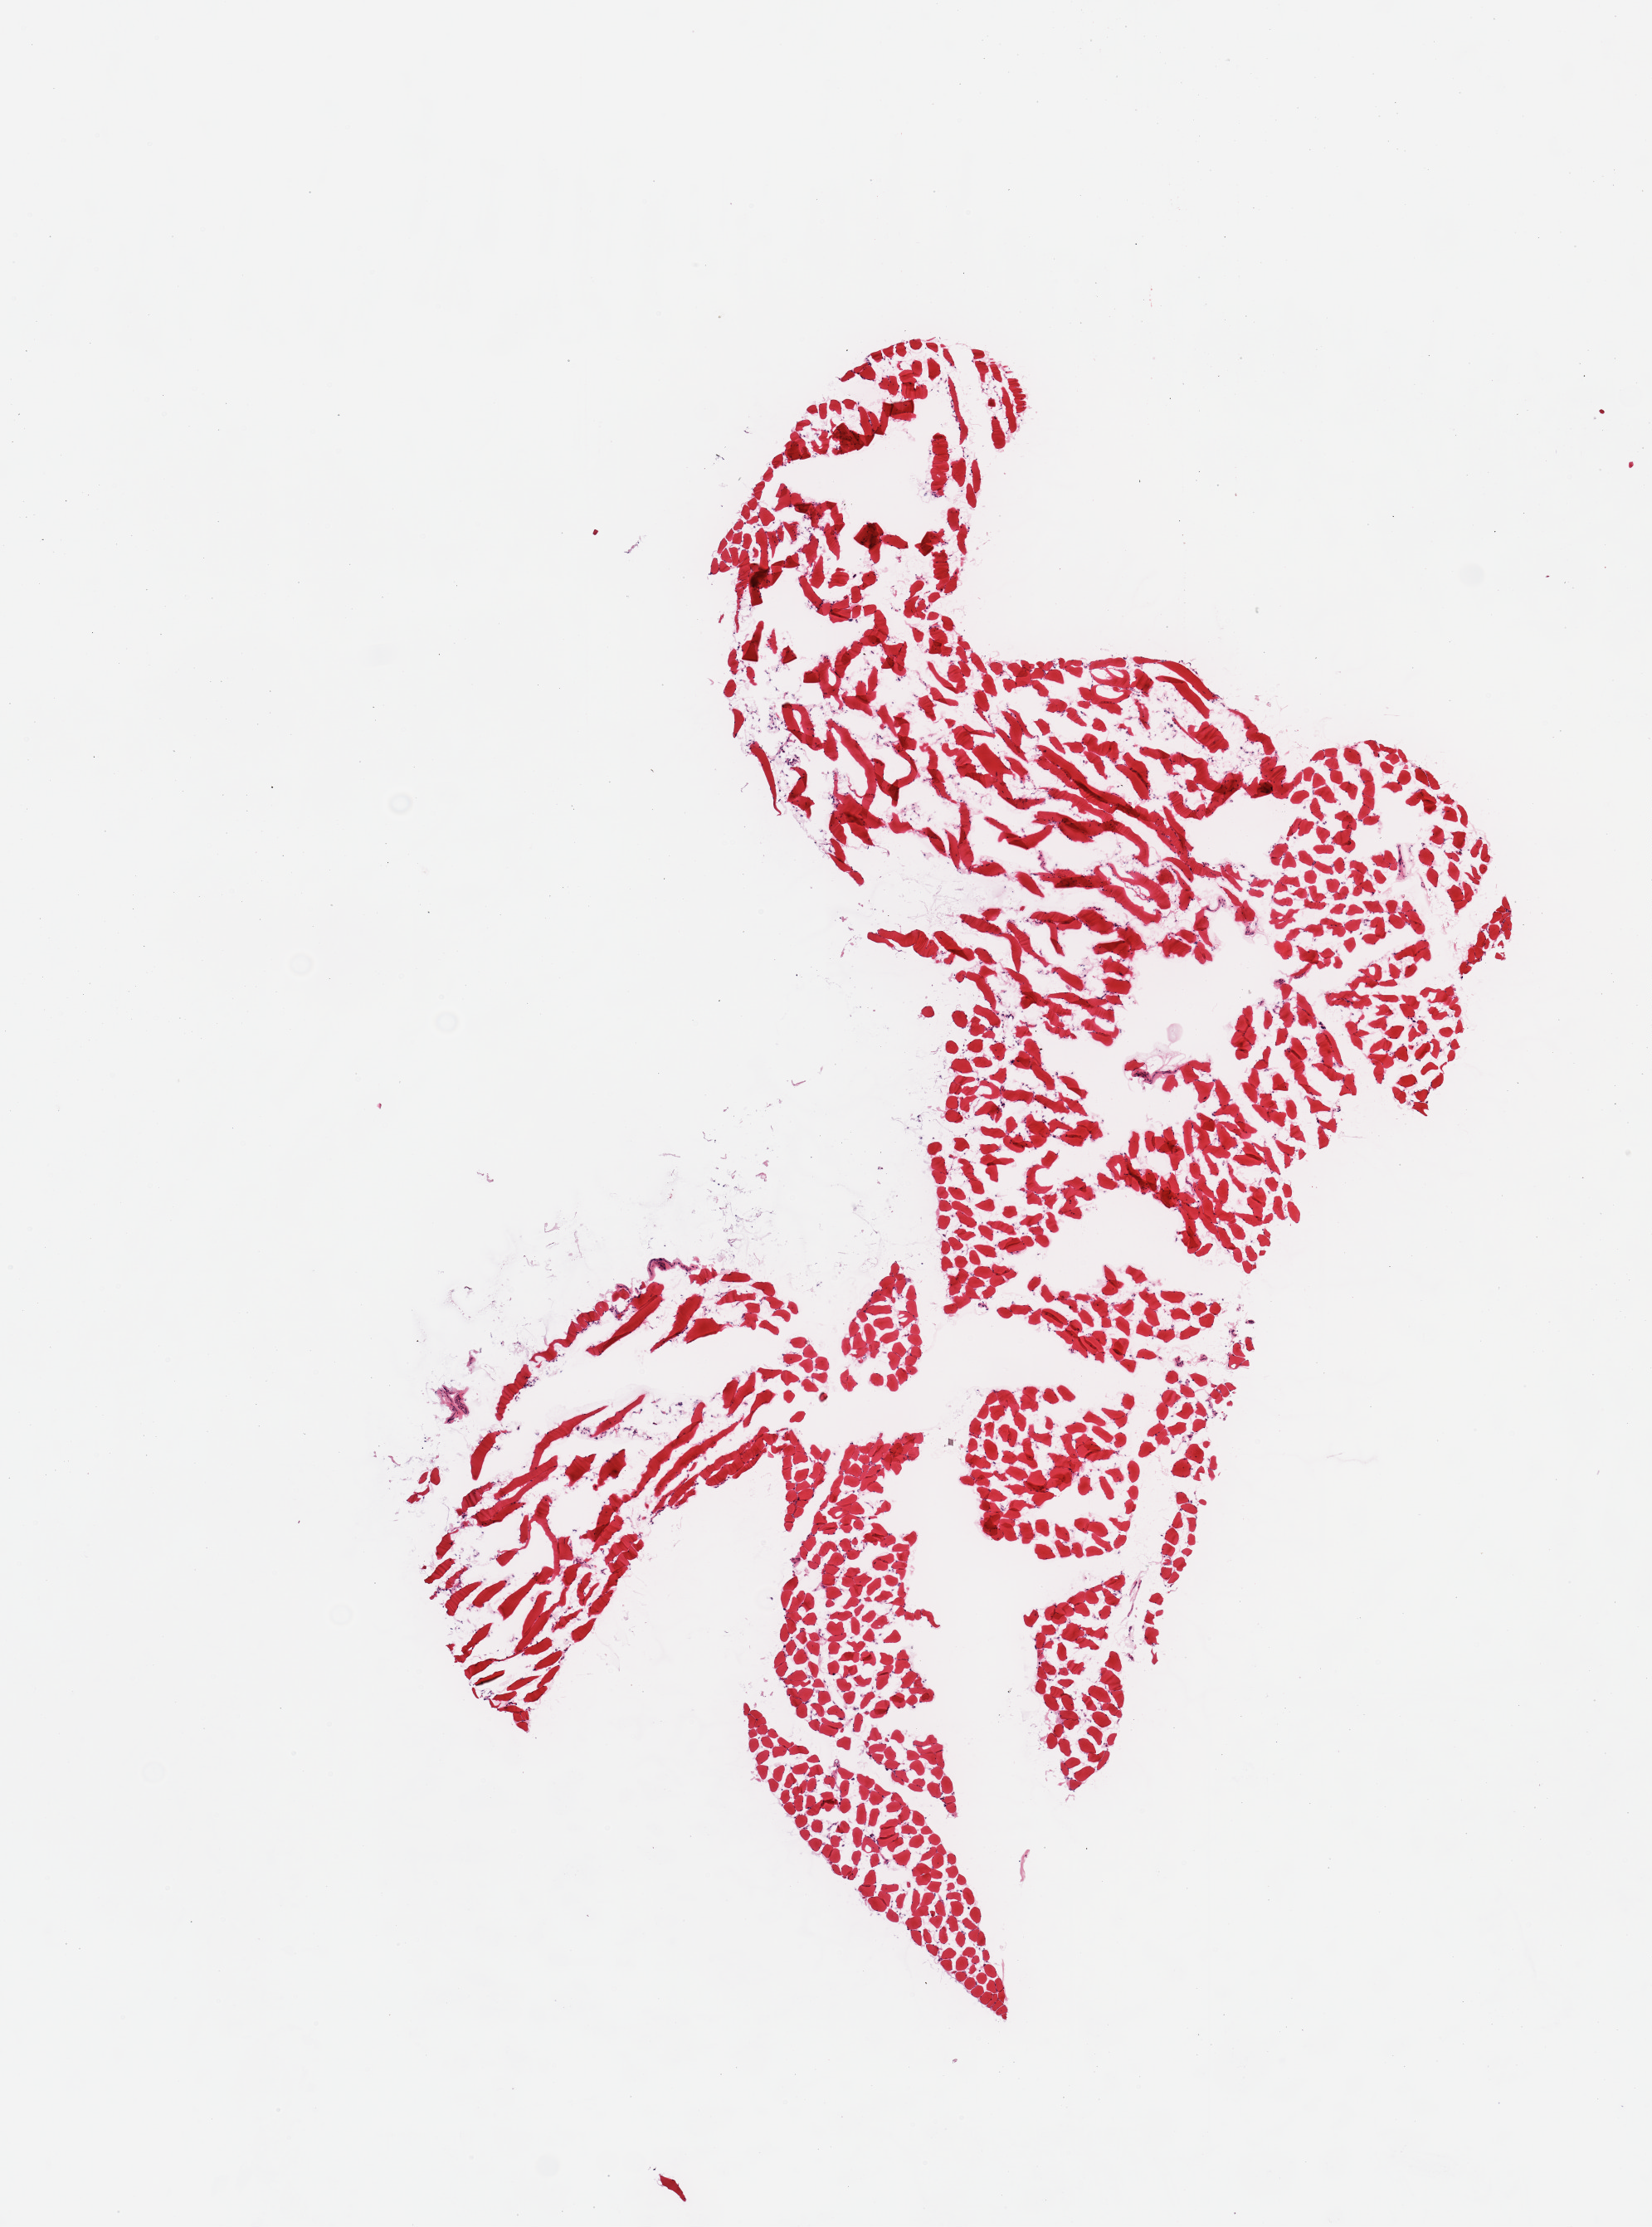
Hematoxylin and eosin (H&E) whole-slide image, shown as a low-resolution overview of the whole scanned area (about 7.9 x 10.6 mm). Male donor.
Specimen: frozen section; sampled site (target tissue): skeletal muscle; tissue donor sample.